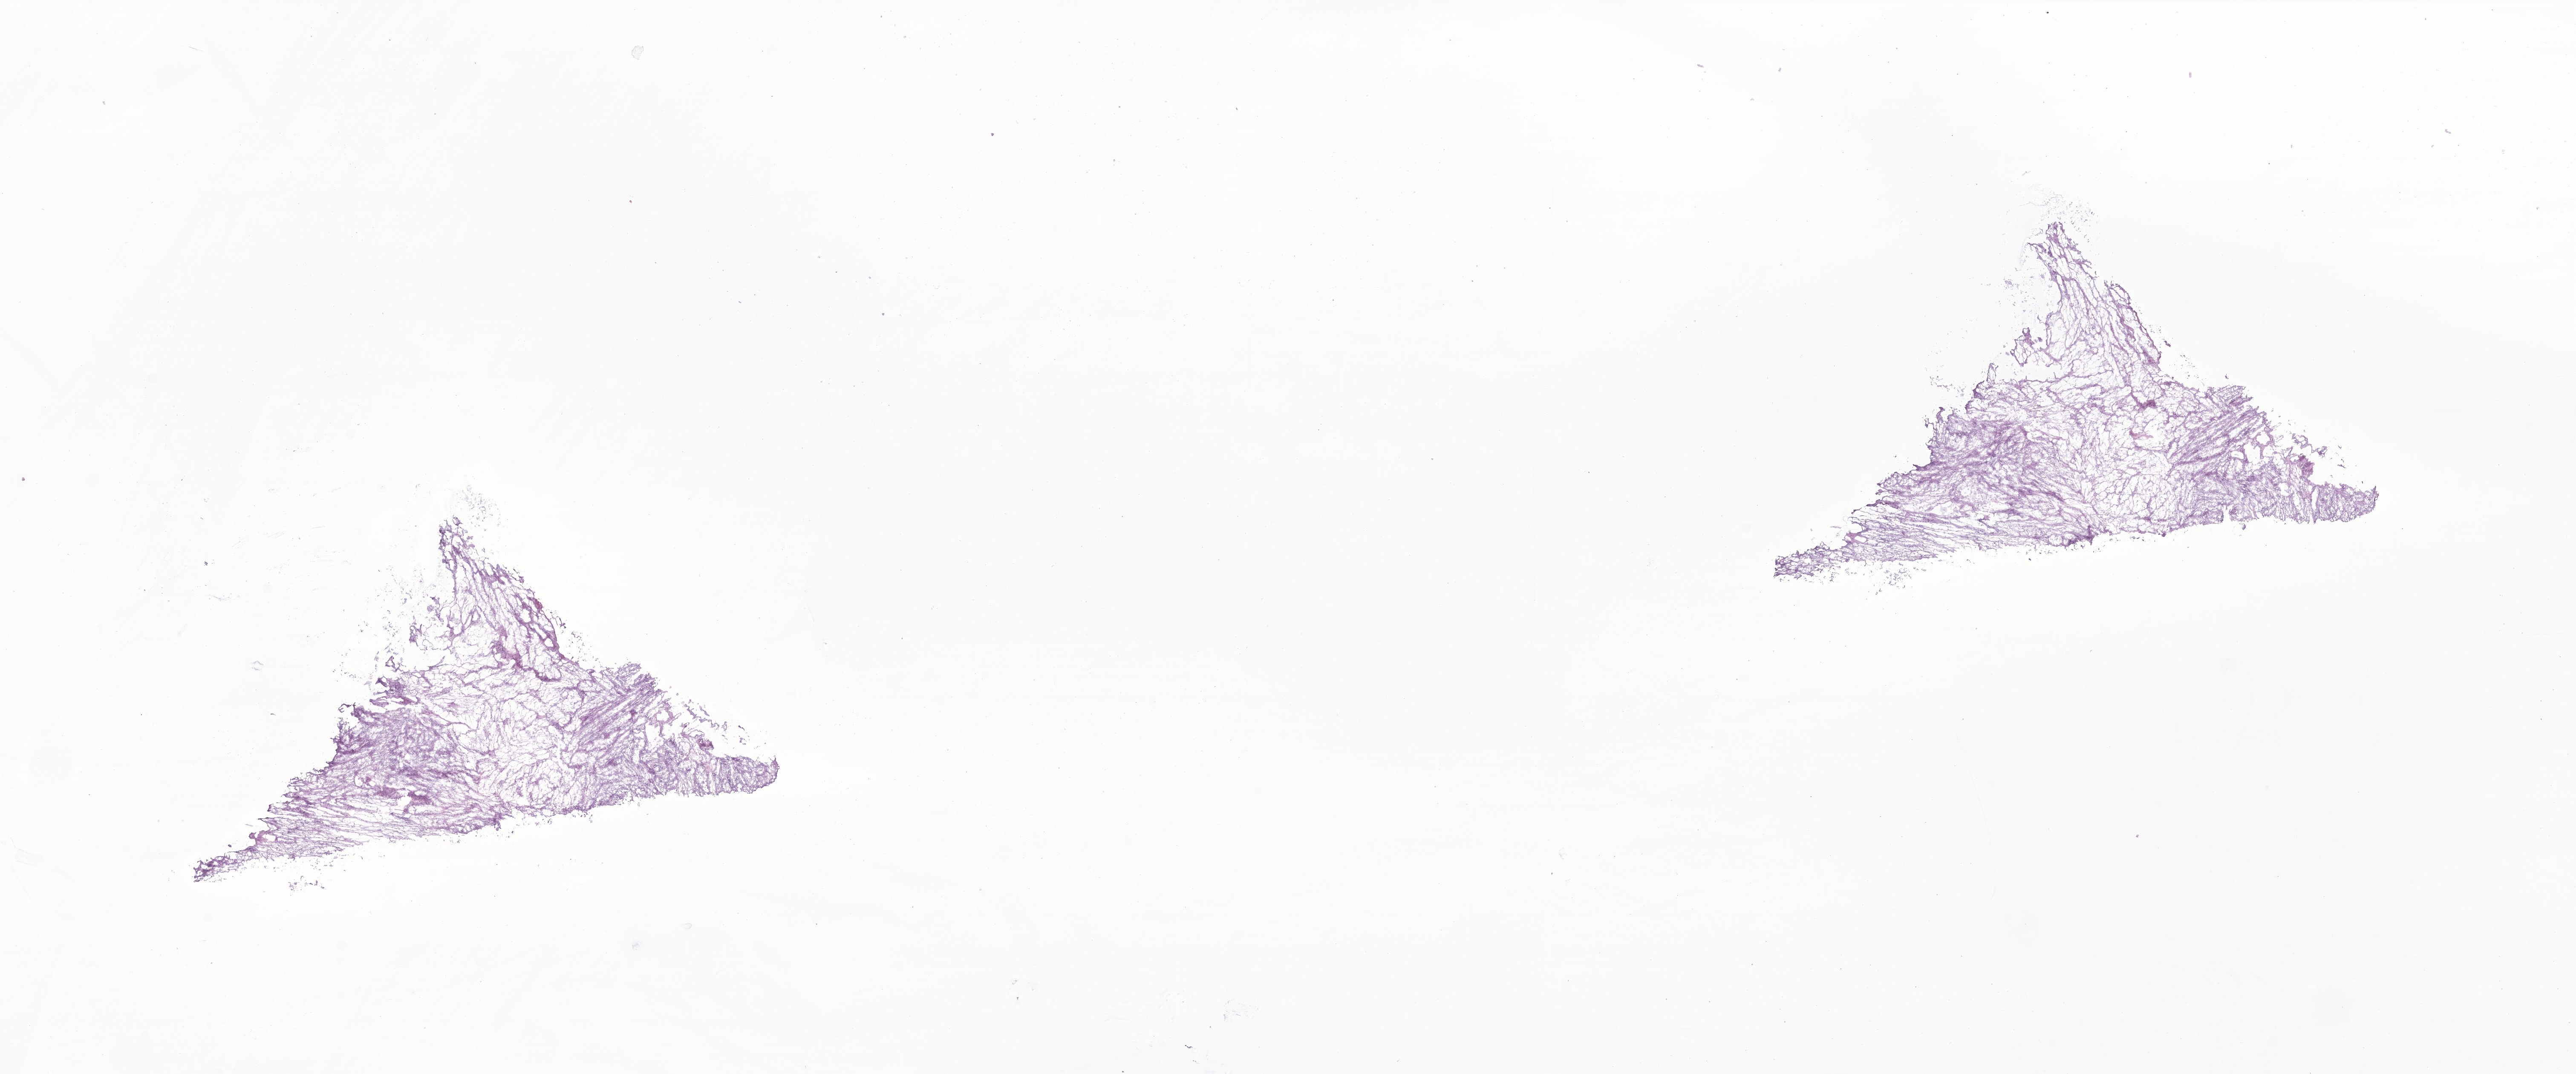
Haematoxylin and eosin whole-slide image of tumor tissue from the spinal cord, a low-resolution overview of the entire scanned area, about 25.5 x 10.6 mm, frozen section. Patient: female, age 186 months (15 years 6 months).
Recorded diagnosis: Schwannoma, NOS.